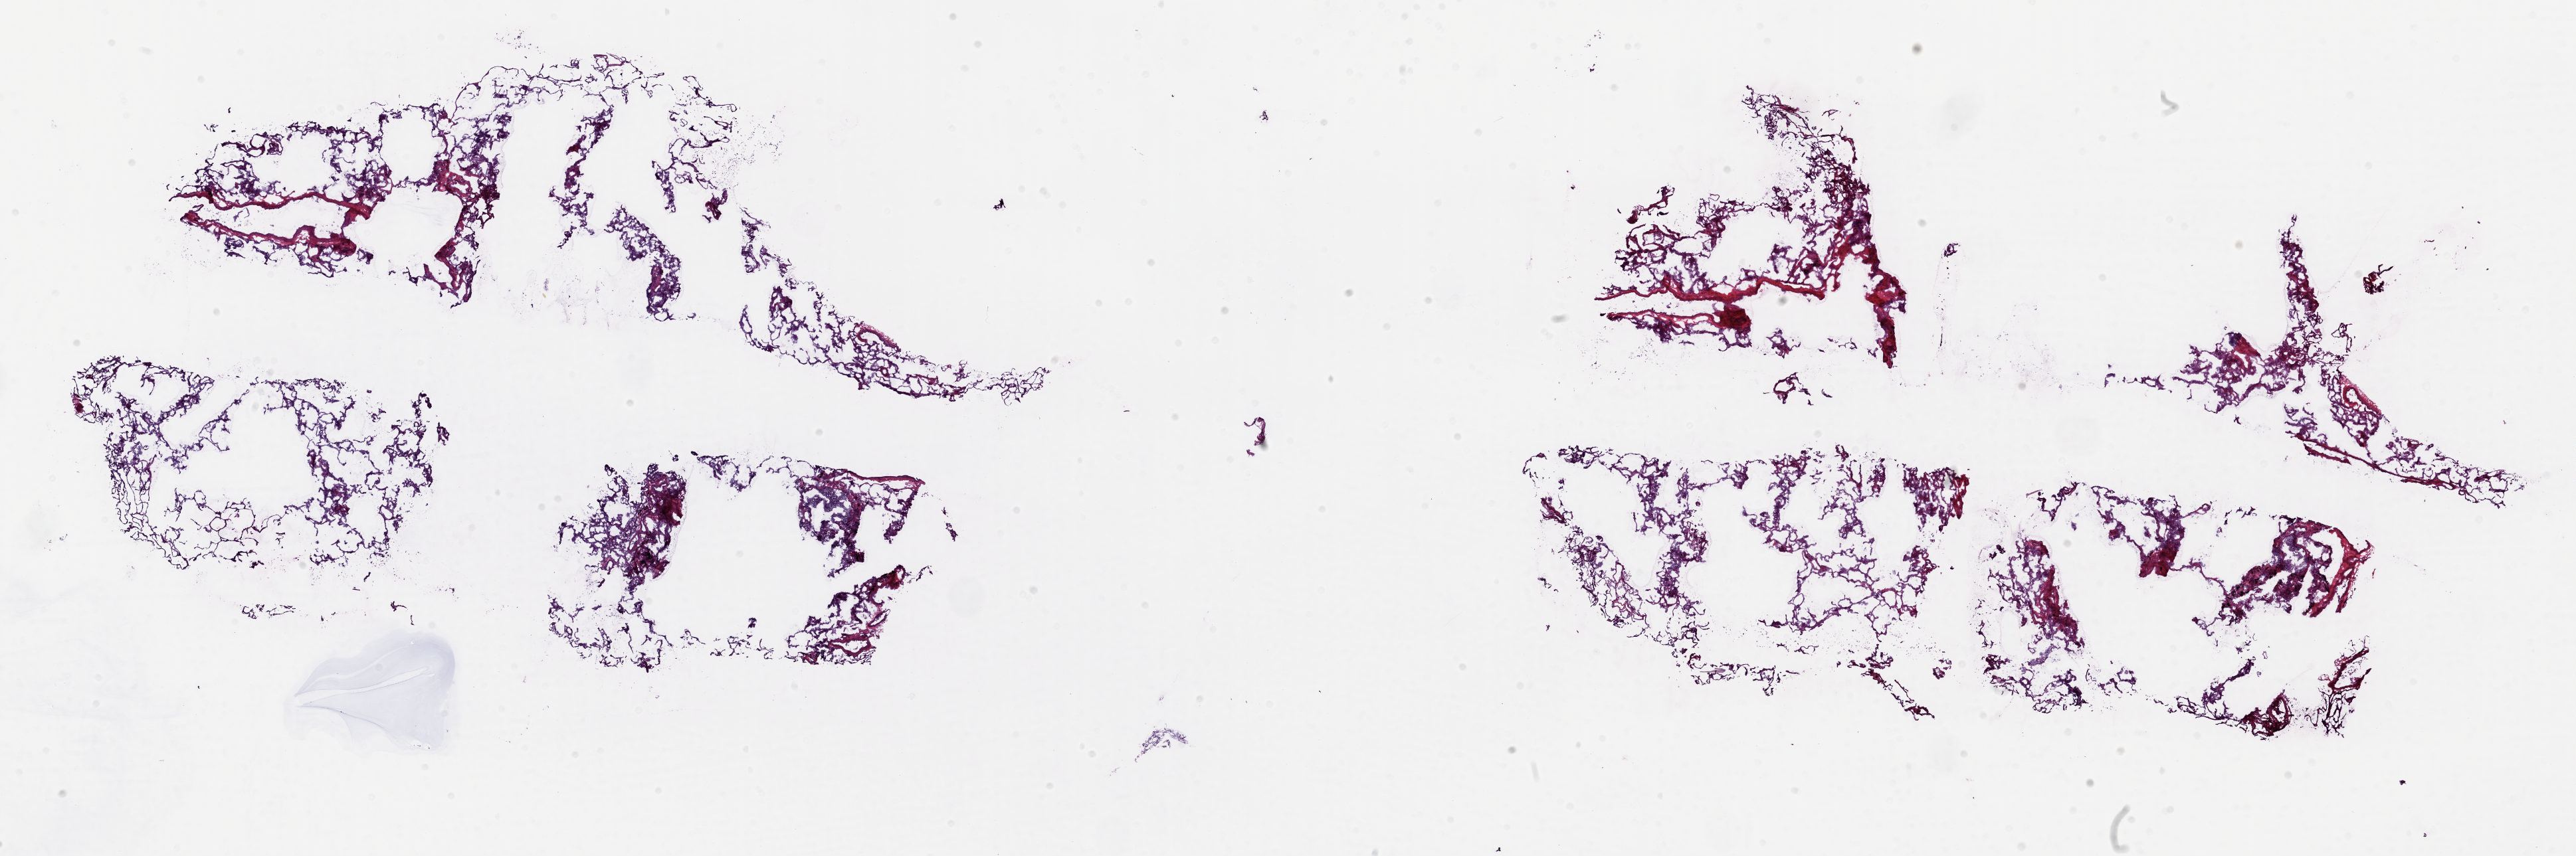
Digitized H&E-stained tissue section (whole slide), low-resolution overview of the scanned area, about 30.7 x 10.2 mm; frozen section; sample: solid tissue normal (non-tumour tissue), lung. Female patient; age at initial diagnosis 59 years. Composition of this section per pathologist review: tumour cells 0%, tumour nuclei 0%, normal cells 90%, stromal cells 10%, necrosis 0%. Infiltration values recorded for this section: lymphocyte infiltration 5%, monocyte infiltration 15%, neutrophil infiltration 0%.
• this section: solid tissue normal sample (biorepository sample class)
• patient diagnosis: Squamous cell carcinoma, NOS